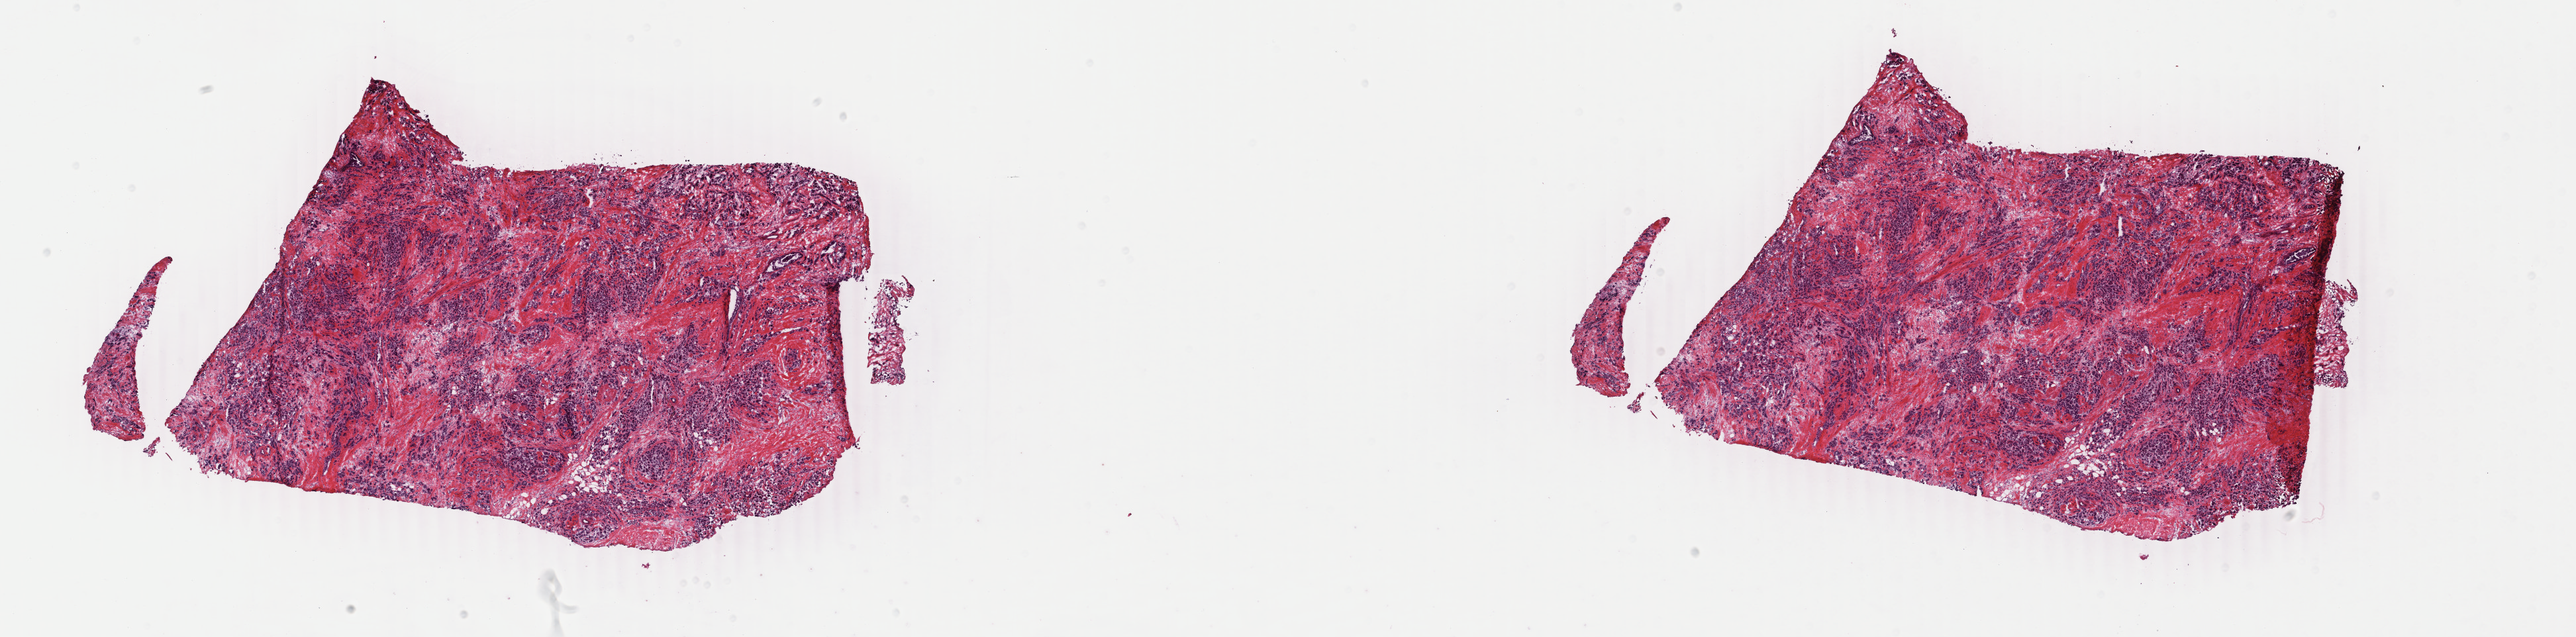
Whole-slide histology image, H&E-stained, low-resolution overview of the scanned area, about 30.9 x 7.7 mm (from a 40x scan), frozen section, breast, primary tumour sample. Patient: female, age at initial diagnosis 46 years. Composition of this section per pathologist review: tumour cells 90%, tumour nuclei 90%, normal cells 0%, stromal cells 10%, necrosis 0%. Inflammatory infiltration, as recorded: lymphocyte infiltration 1%, monocyte infiltration 0%, neutrophil infiltration 0%.
* histologic diagnosis: Infiltrating duct carcinoma, NOS
* laterality: right